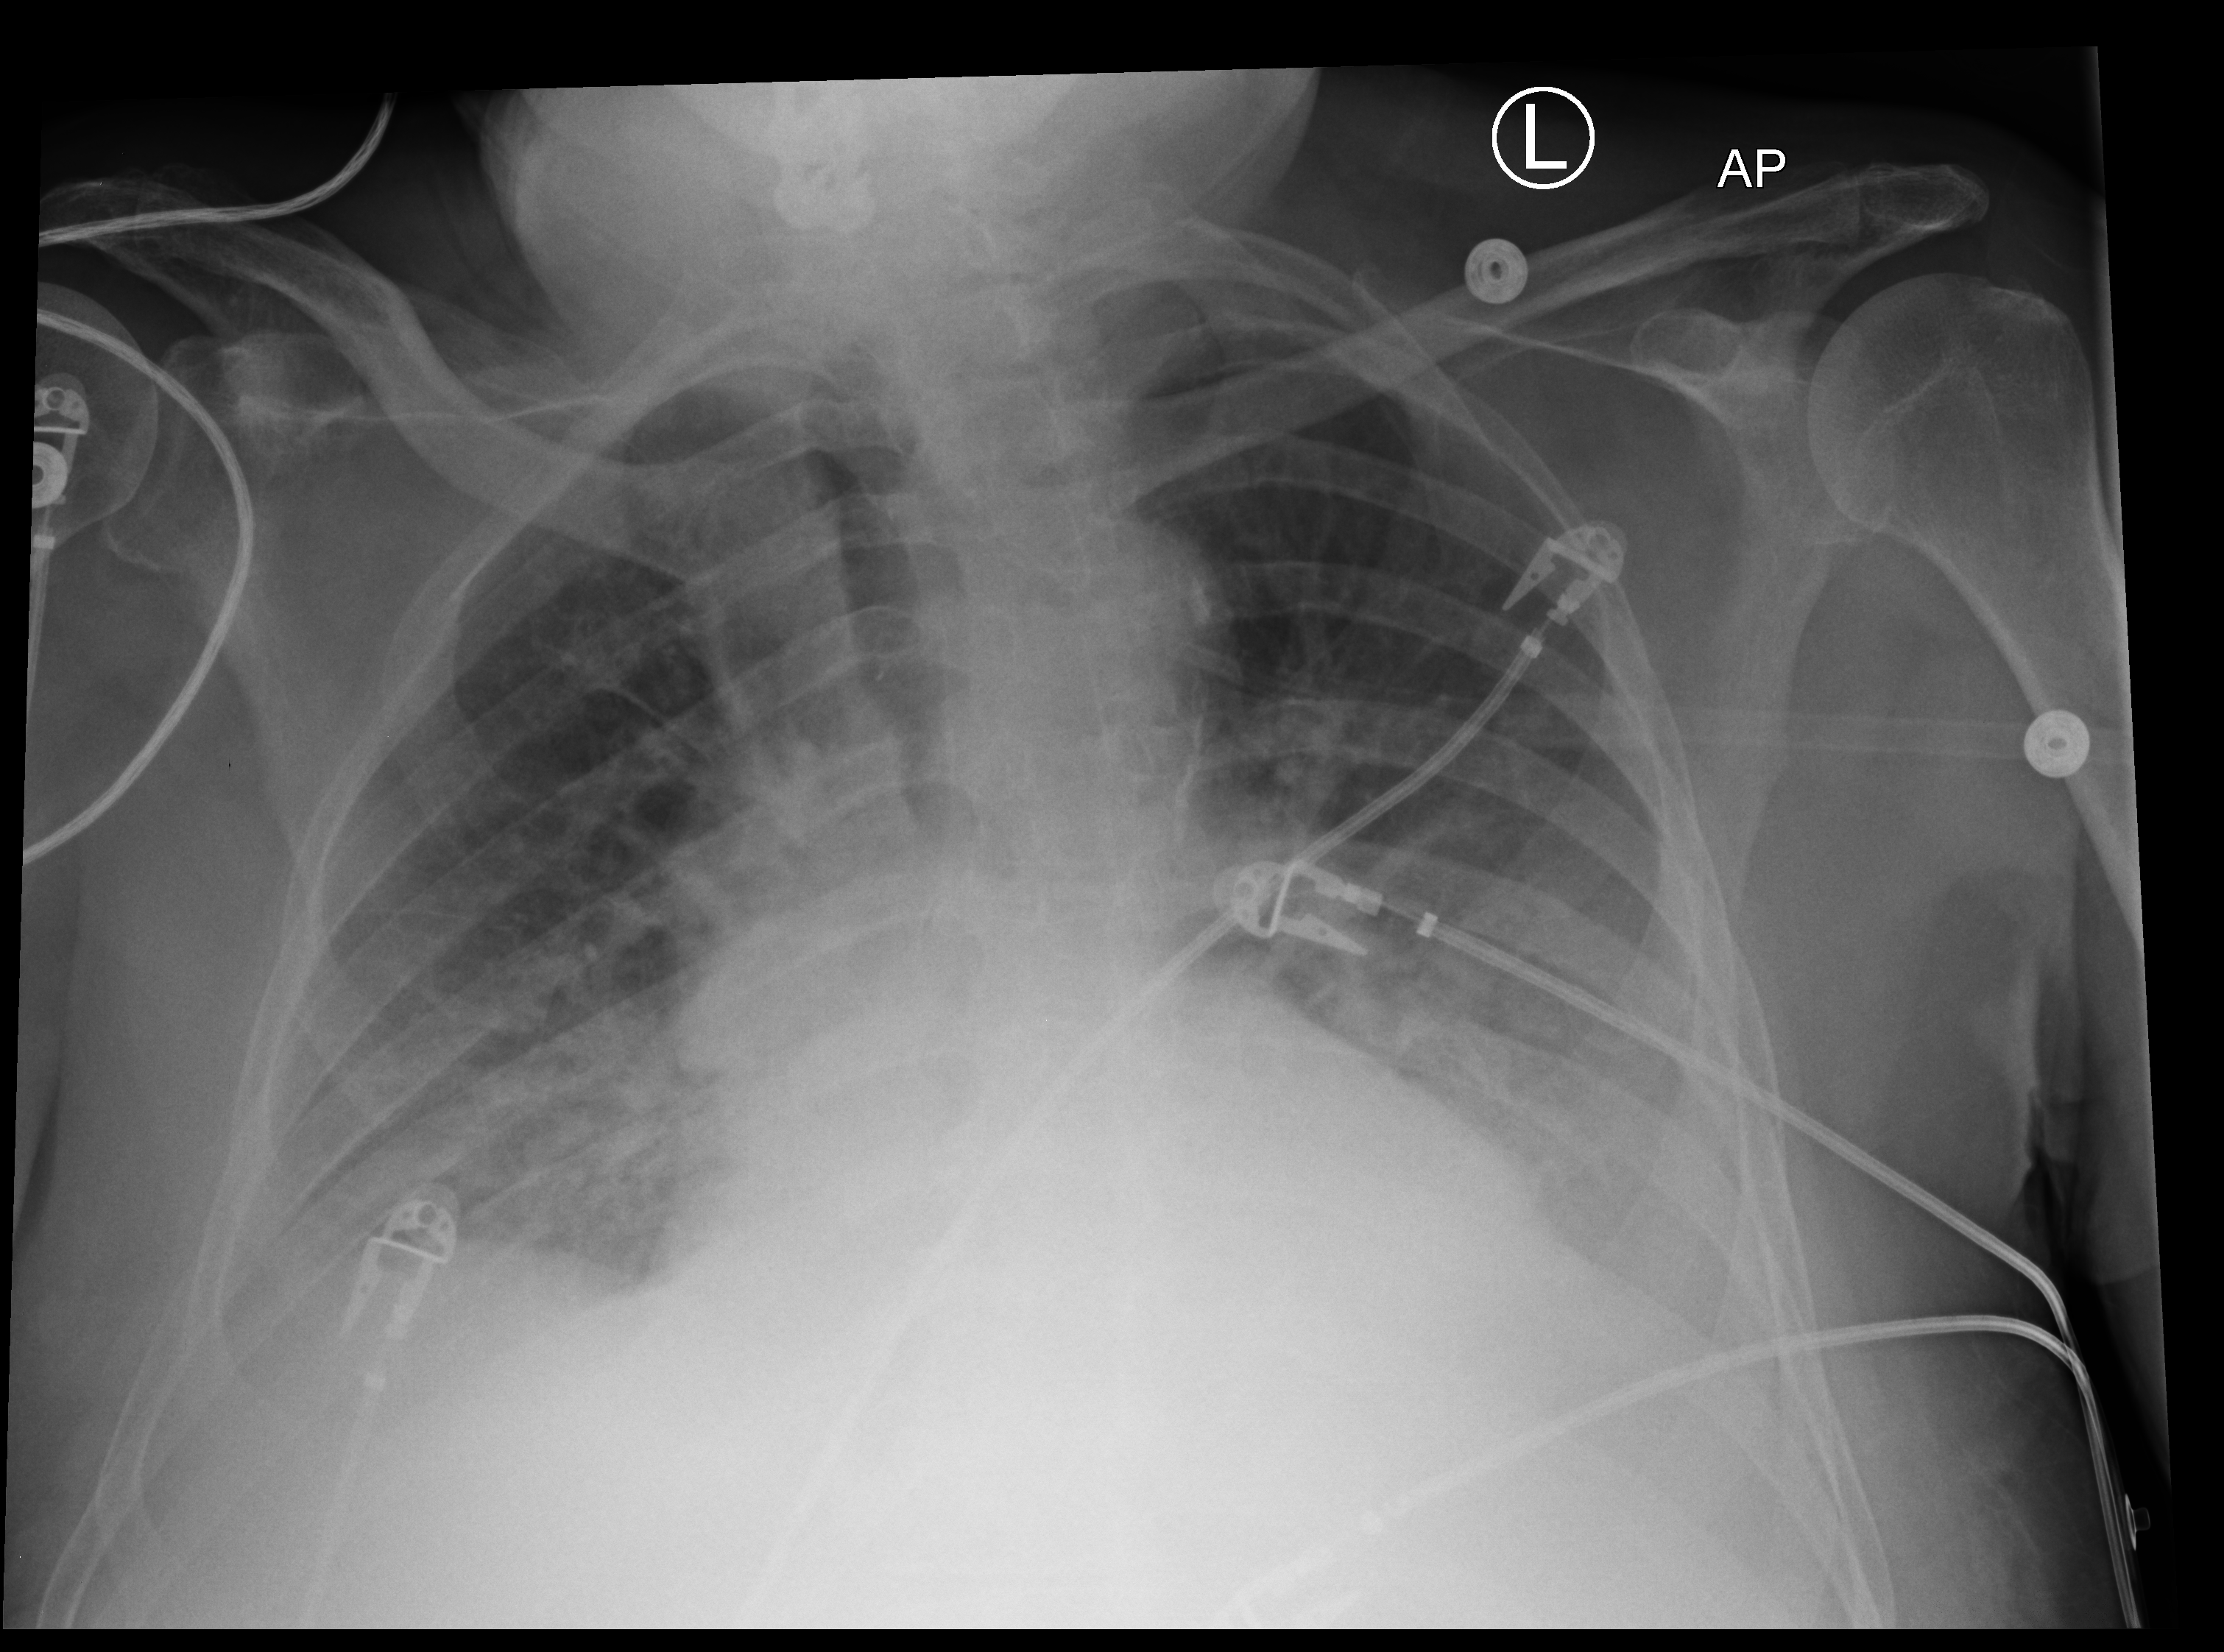
Portable chest radiograph. Patient hospitalised with COVID-19; male, aged 75–90 years.
From the hospital-stay record, not from the radiograph (when in the stay this image was taken is not recorded):
- admitted to intensive care during this hospital stay: yes